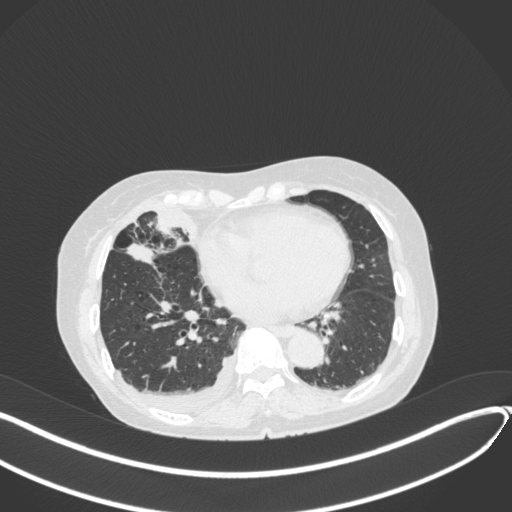
Chest CT, one axial slice; position 149 of 418 along the scan axis; reconstruction kernel B31f; lung window (W 1500 / L -600 HU); 512 × 512 image matrix. Patient: female, 75 years. Case-level facts recorded for this patient, not image findings: clinical TNM (as recorded): T2a N3 M0.
Annotated regions visible in this slice (rectangle marked by the reading radiologist):
- lung tumour (recorded histology: adenocarcinoma): bounding box [x1, y1, x2, y2] px = [126, 243, 161, 269]